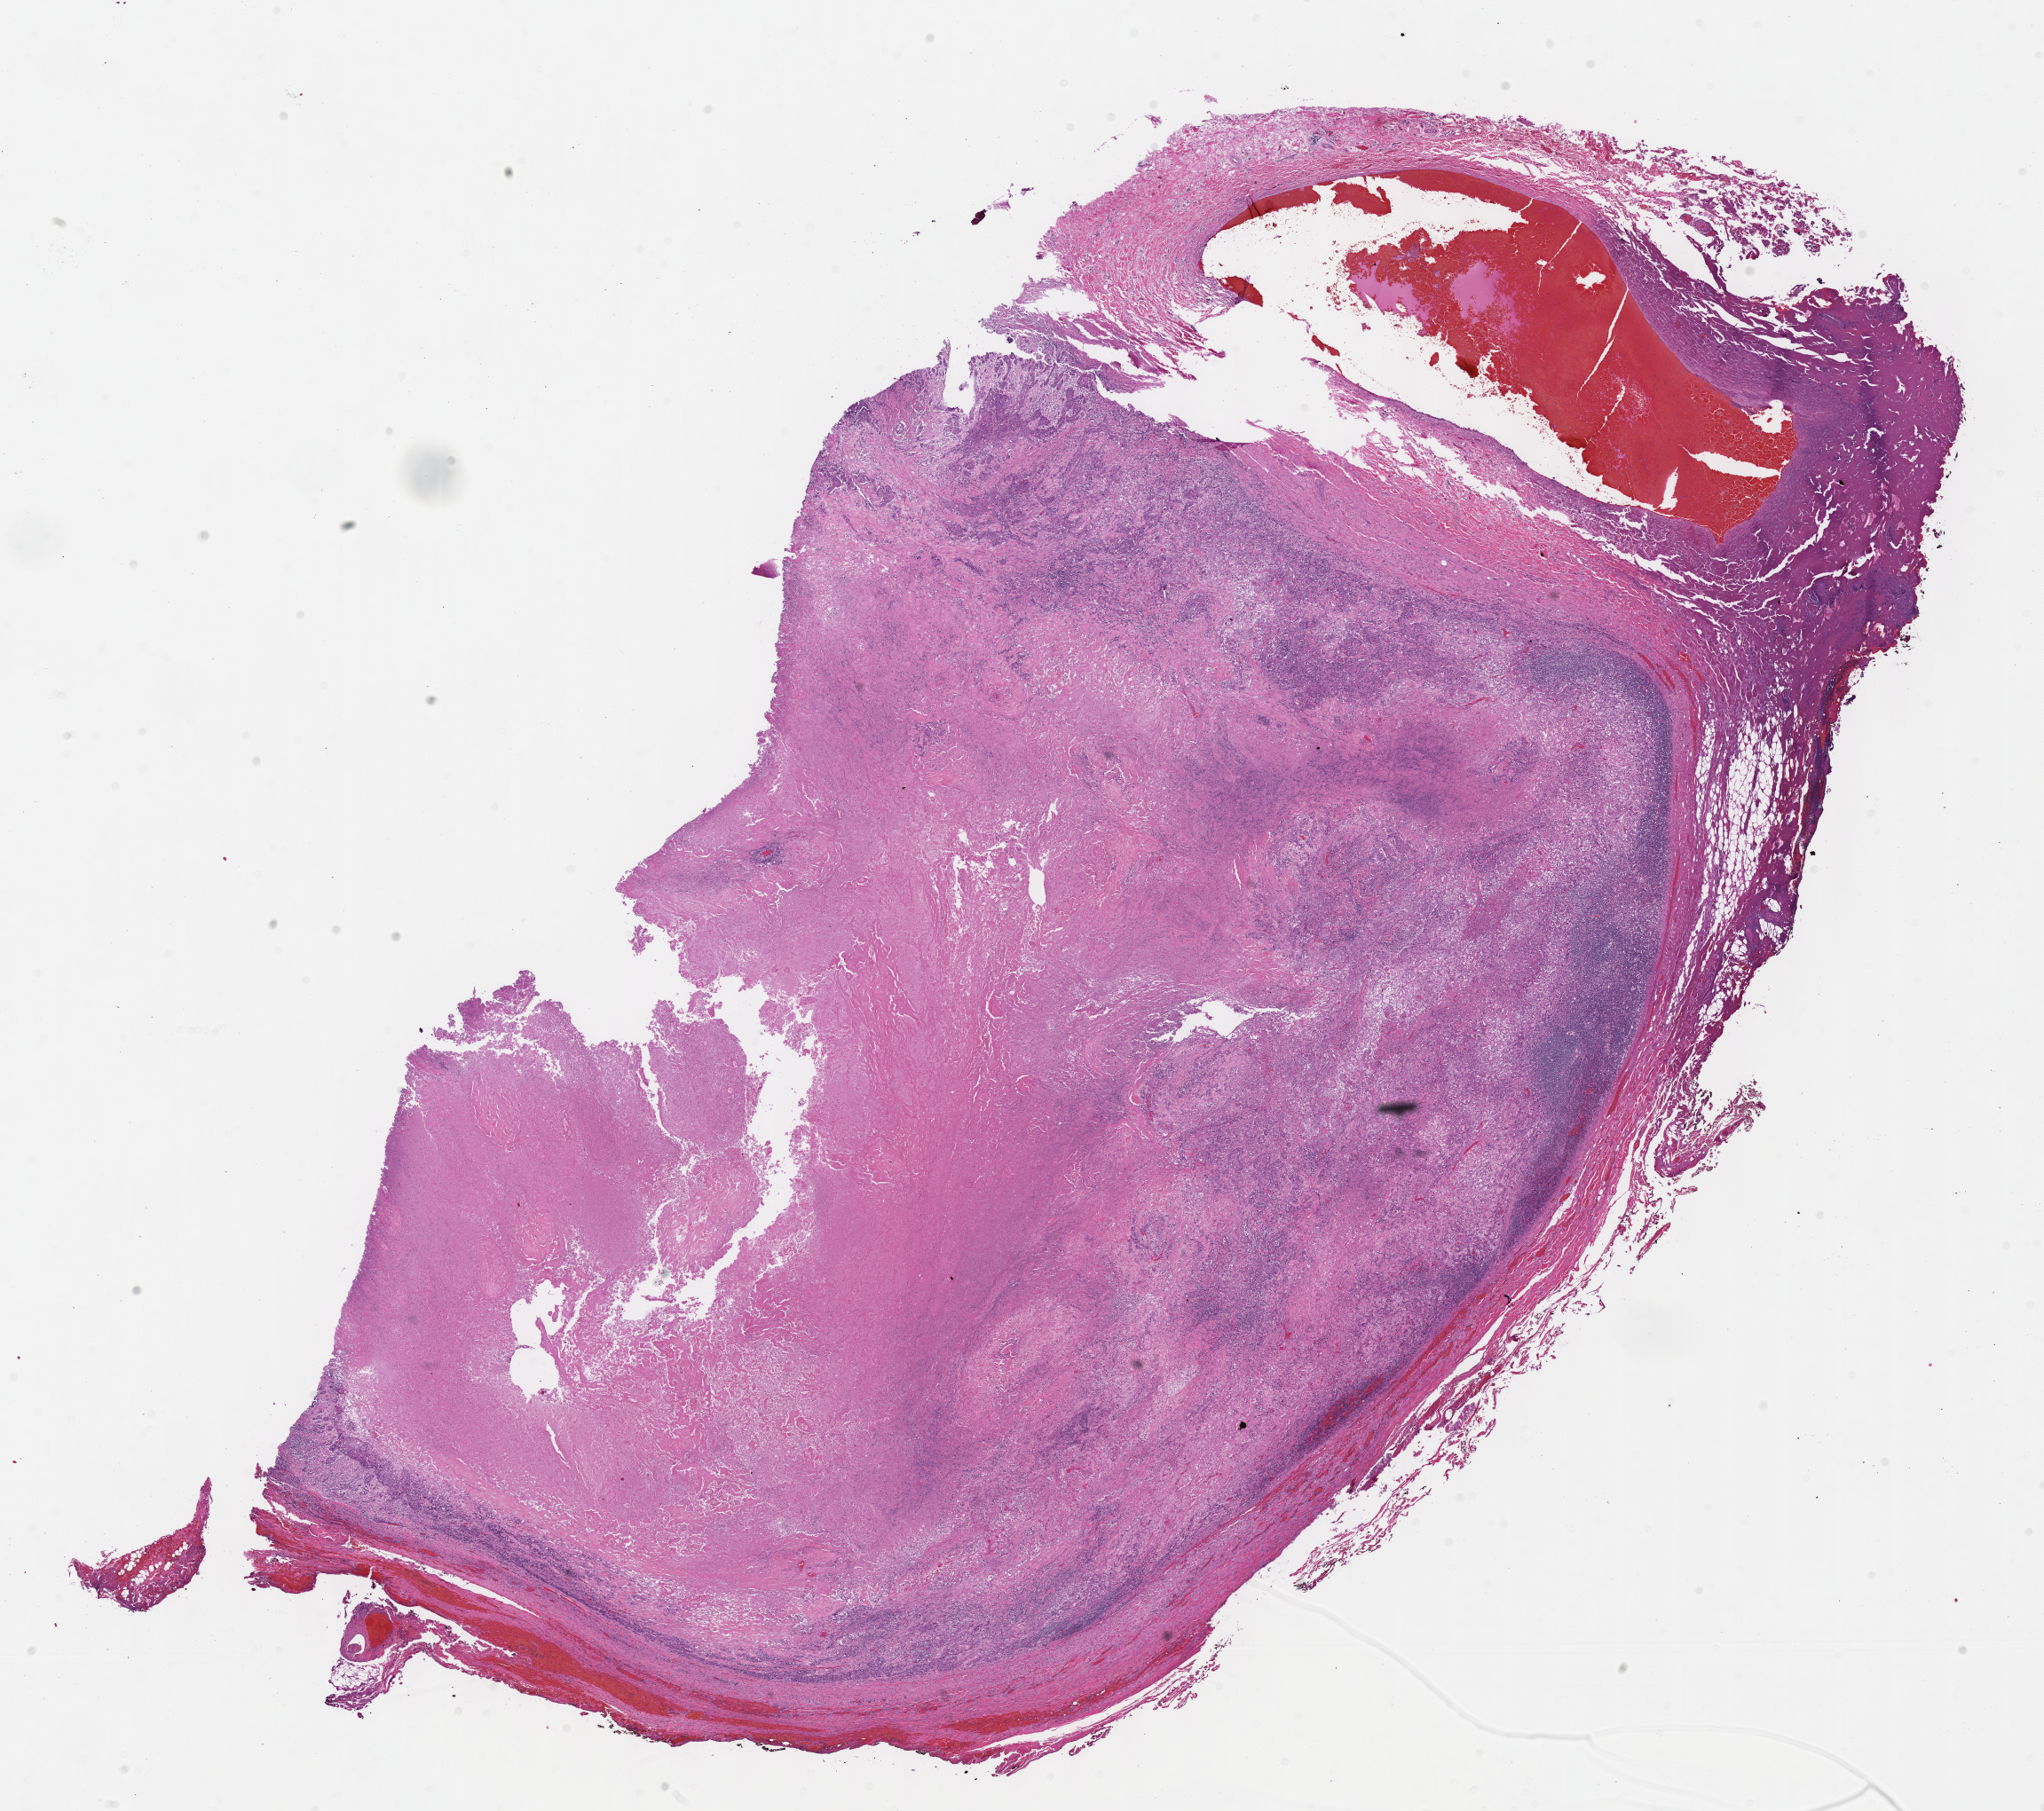
Digitized Hematoxylin and eosin (H&E) stained tissue section (whole slide), low-resolution overview of the scanned area, about 18.6 x 16.5 mm (slide scanned at 40x). Formalin-fixed paraffin-embedded (FFPE) diagnostic section. Sample: primary tumour, head and neck. Patient: male, age at initial diagnosis 47 years.
Diagnosis: Squamous cell carcinoma, NOS (mouth, NOS).